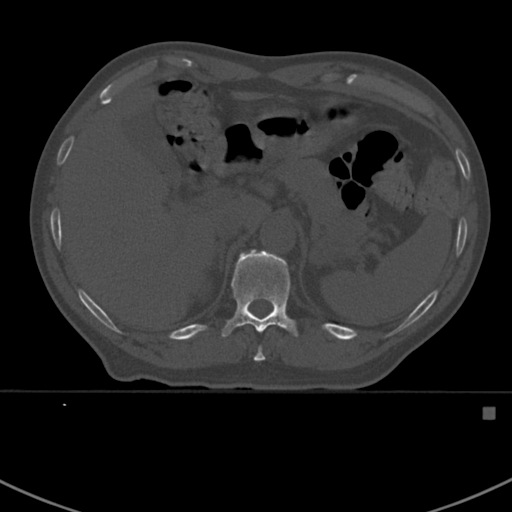
CT including the spine, one axial slice; position 349 of 412 along the scan axis; reconstruction kernel Br40s; 120 kVp; bone window (W 1800 / L 400 HU); 1.5 mm slice thickness; 512 × 512 image matrix, field of view 358 × 358 mm. Male patient, age 59 years. From the clinical record (not read from this slice): primary cancer: prostate.
Structures marked on this image (semi-automatically segmented with operator editing):
- T10 vertebra: bounding box <254,347,265,362> (left, top, right, bottom; pixels)
- T11 vertebra: <221,249,299,338>